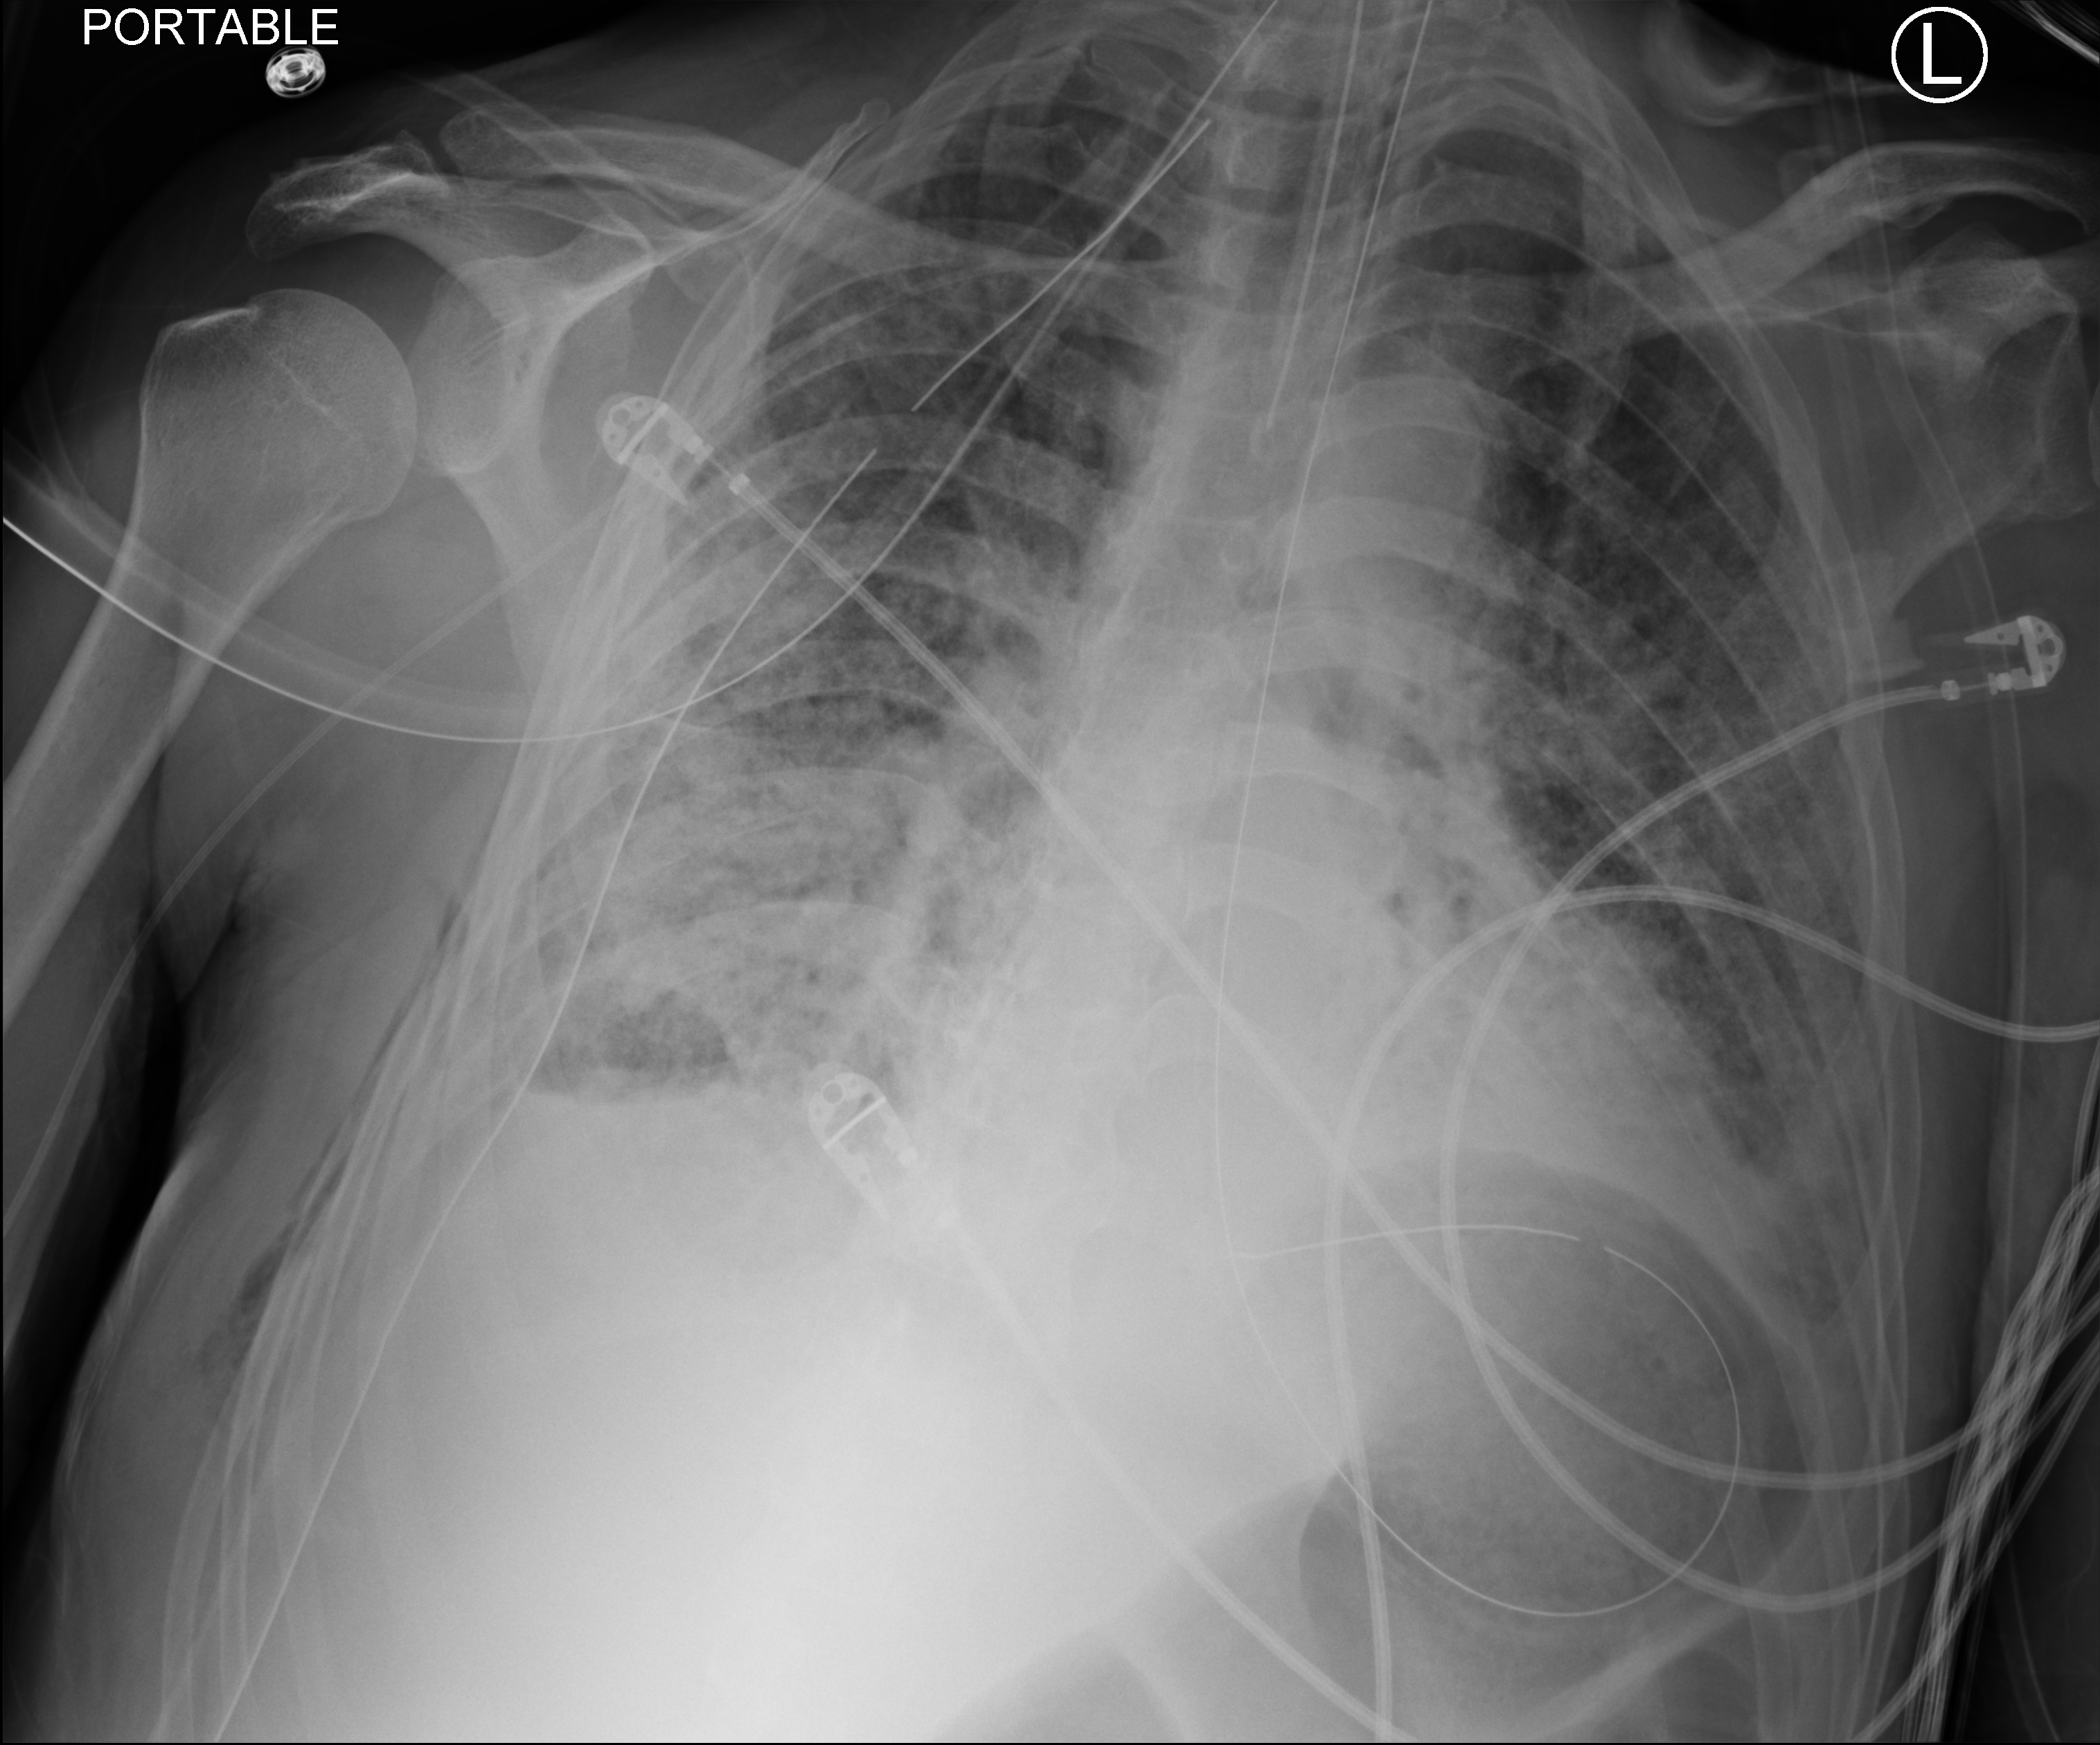
Chest X-ray (portable), anteroposterior (AP) projection. Patient hospitalised with COVID-19; male, aged 60–74 years.
Hospital-stay facts (about this admission, not read from this image; timing relative to this image not recorded): admitted to intensive care during this hospital stay: yes; hypertension (admission record): yes; mechanically ventilated during this hospital stay: yes.